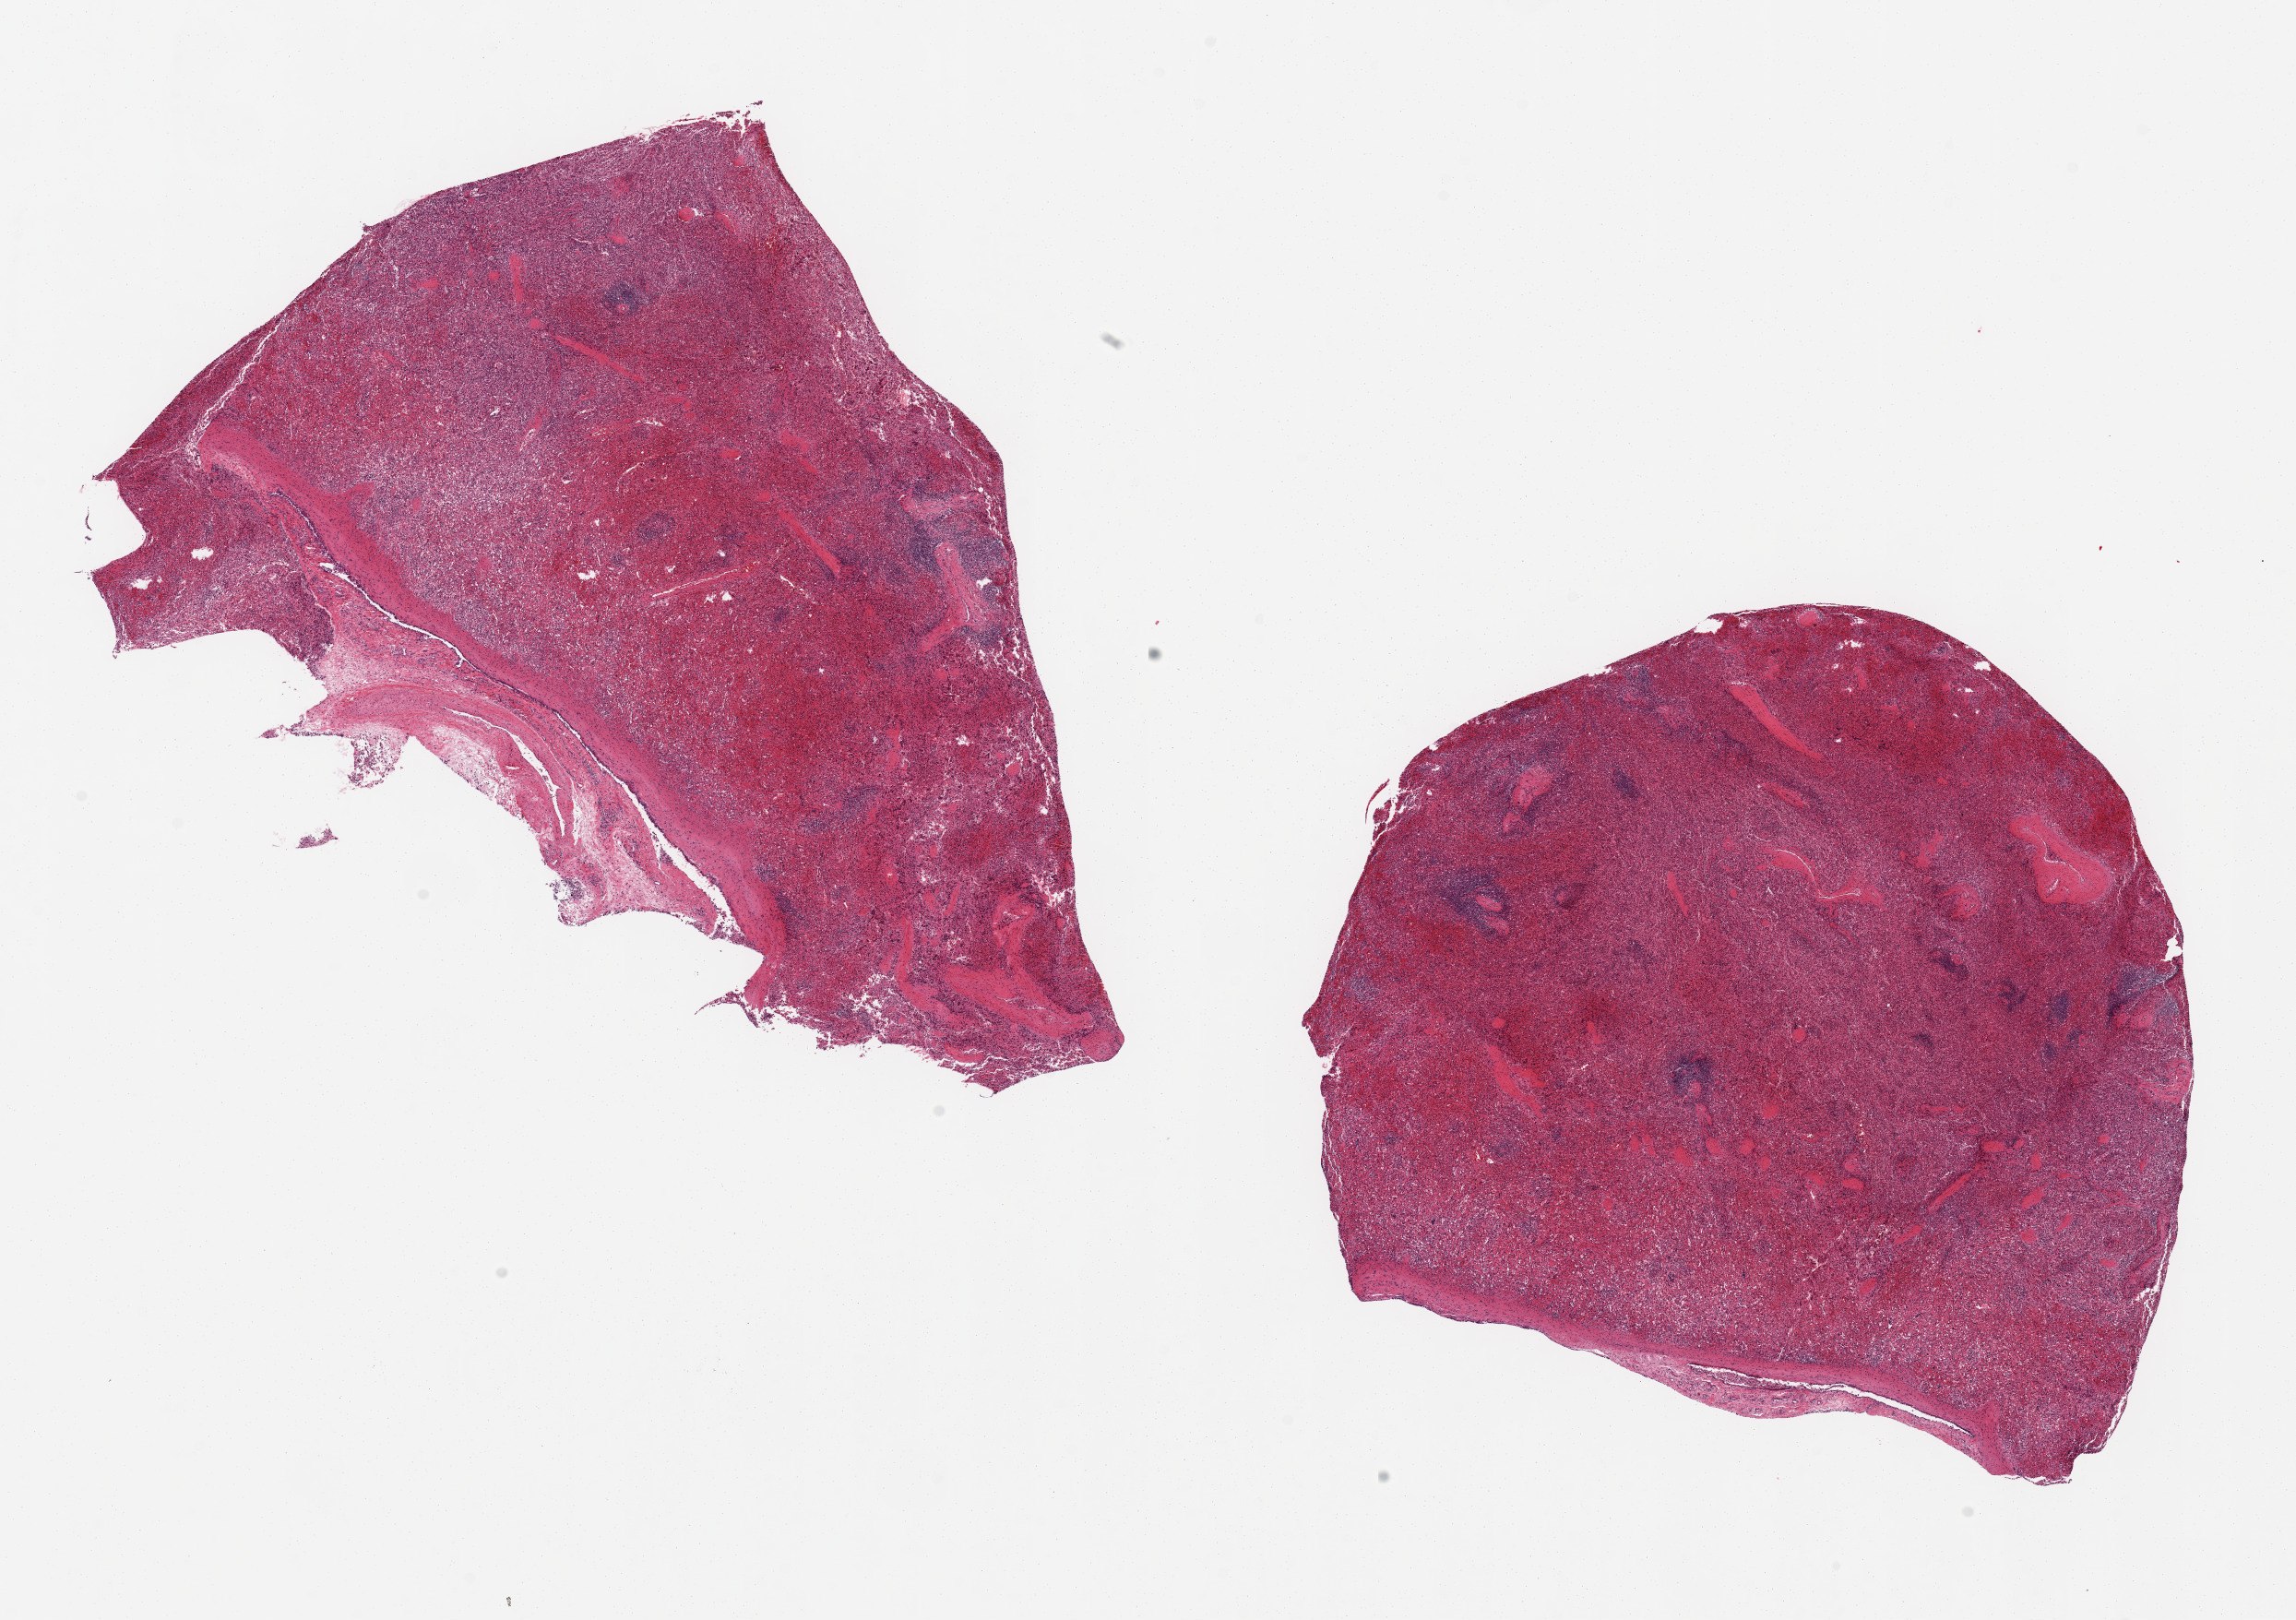
Haematoxylin and eosin whole-slide image, whole scanned area (about 19.7 x 13.9 mm, slide scanned at 20x) shown as a low-resolution overview. PAXgene-fixed paraffin-embedded (PFPE) section. Sampled site (target tissue): spleen. Donor tissue sample. Female donor.
Reviewer comment on this tissue sample: 2 ~7.5x6.5mm aliquots, foci of adherent extraspenic vascular/fibrous tissue present (~4x1mm).